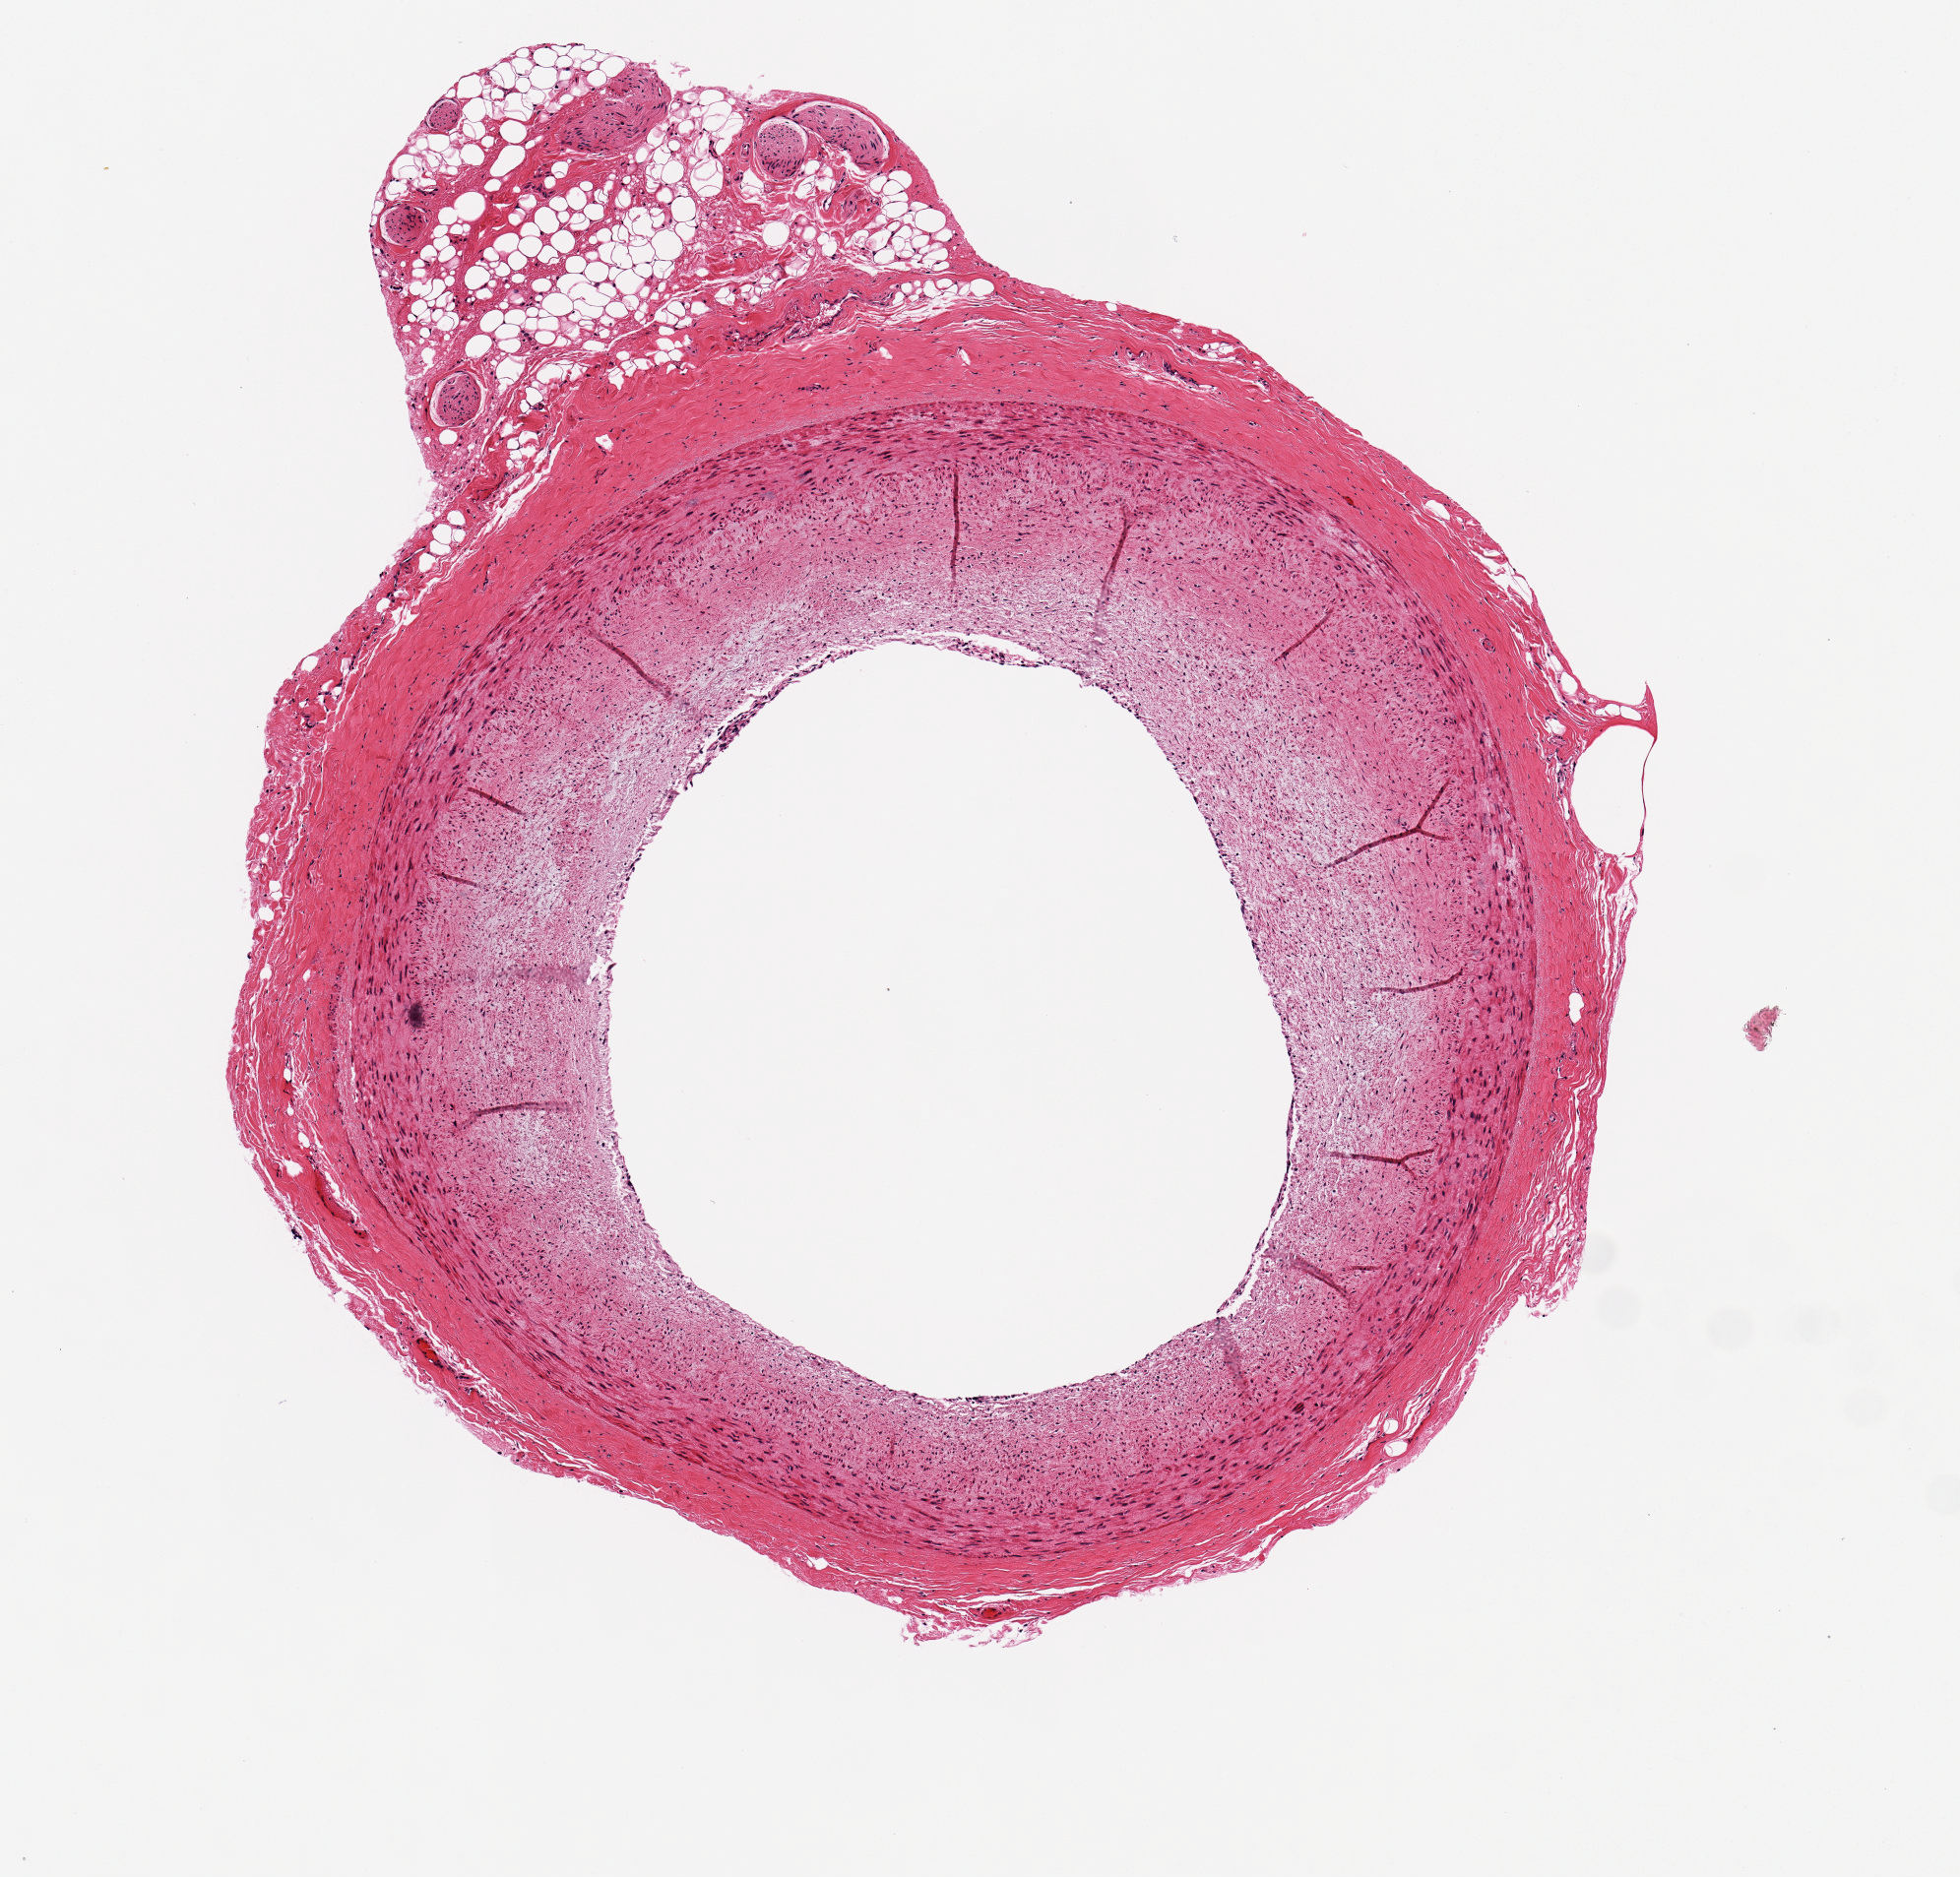
Hematoxylin and eosin (H&E) whole-slide image — whole scanned area (about 3.9 x 3.8 mm) shown as a low-resolution overview; PAXgene-fixed, paraffin-embedded tissue; target tissue: coronary artery; tissue donor sample. Male donor.
- pathologist's review note for this sample: 2.8x2.9mm. 30% occlusive atherosclerosis. Adherent 1 x 0.5mm nubbin of fat/peripheral nerve tissue